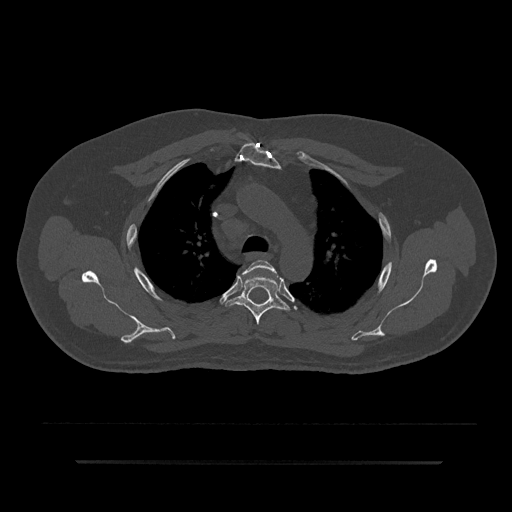
CT including the spine, one axial slice; position 623 of 797 along the scan axis; 120 kVp; bone window (W 1800 / L 400 HU); 0.5 mm slice thickness; 512 × 512 image matrix, field of view 464 × 464 mm. Patient: male, 59 years. From the clinical record (not read from this slice): primary cancer: bile ducts.
Structures marked on this image (semi-automatic segmentation, software-assisted and operator-edited):
- T3 vertebra: box from (x=244, y=260) to (x=281, y=279) px
- T4 vertebra: (x=225, y=271)–(x=290, y=325)